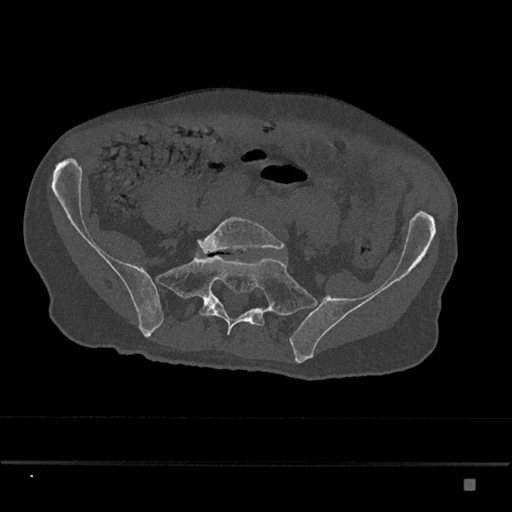
CT including the spine, one axial slice. Position 232 of 797 along the scan axis. 120 kVp. Bone window (W 1800 / L 400 HU). 512 × 512 image matrix, field of view 390 × 390 mm. Male patient, age 72 years. Case-level facts recorded for this patient, not image findings: primary cancer: prostate.
Outlined on this slice (semi-automatically segmented with operator editing):
- L5 vertebra: bounding box <197,216,285,254> (left, top, right, bottom; pixels)